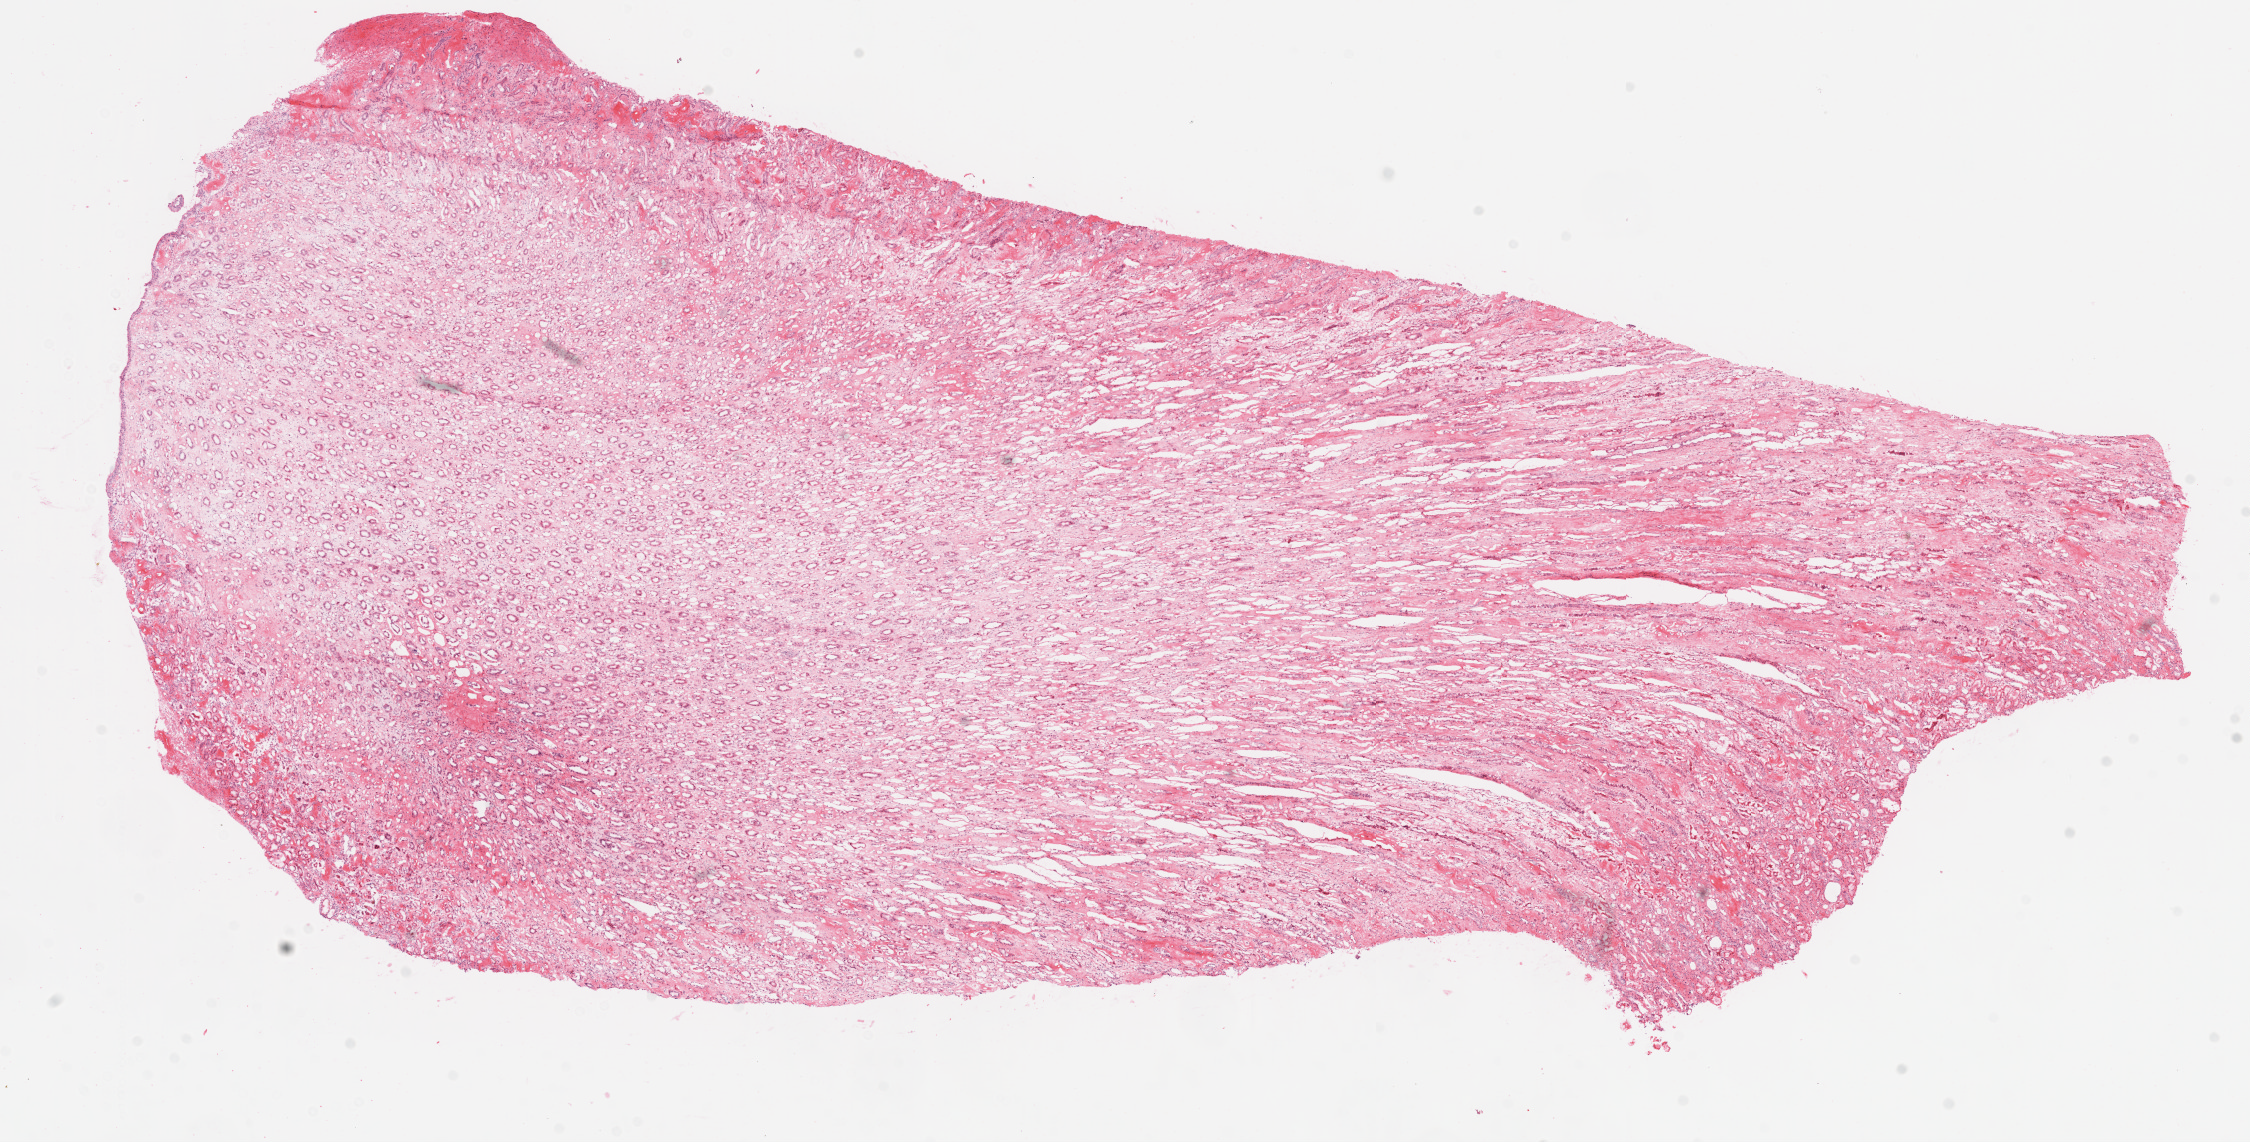
Hematoxylin and eosin (H&E) stained whole-slide image — shown as a low-resolution overview of the whole scanned area (about 18.1 x 9.2 mm); frozen section; solid tissue normal (non-tumour tissue) sample from the kidney. Male, age 84 years at initial diagnosis.
This section: solid tissue normal sample (biorepository sample class). Patient diagnosis: Clear cell adenocarcinoma, NOS.